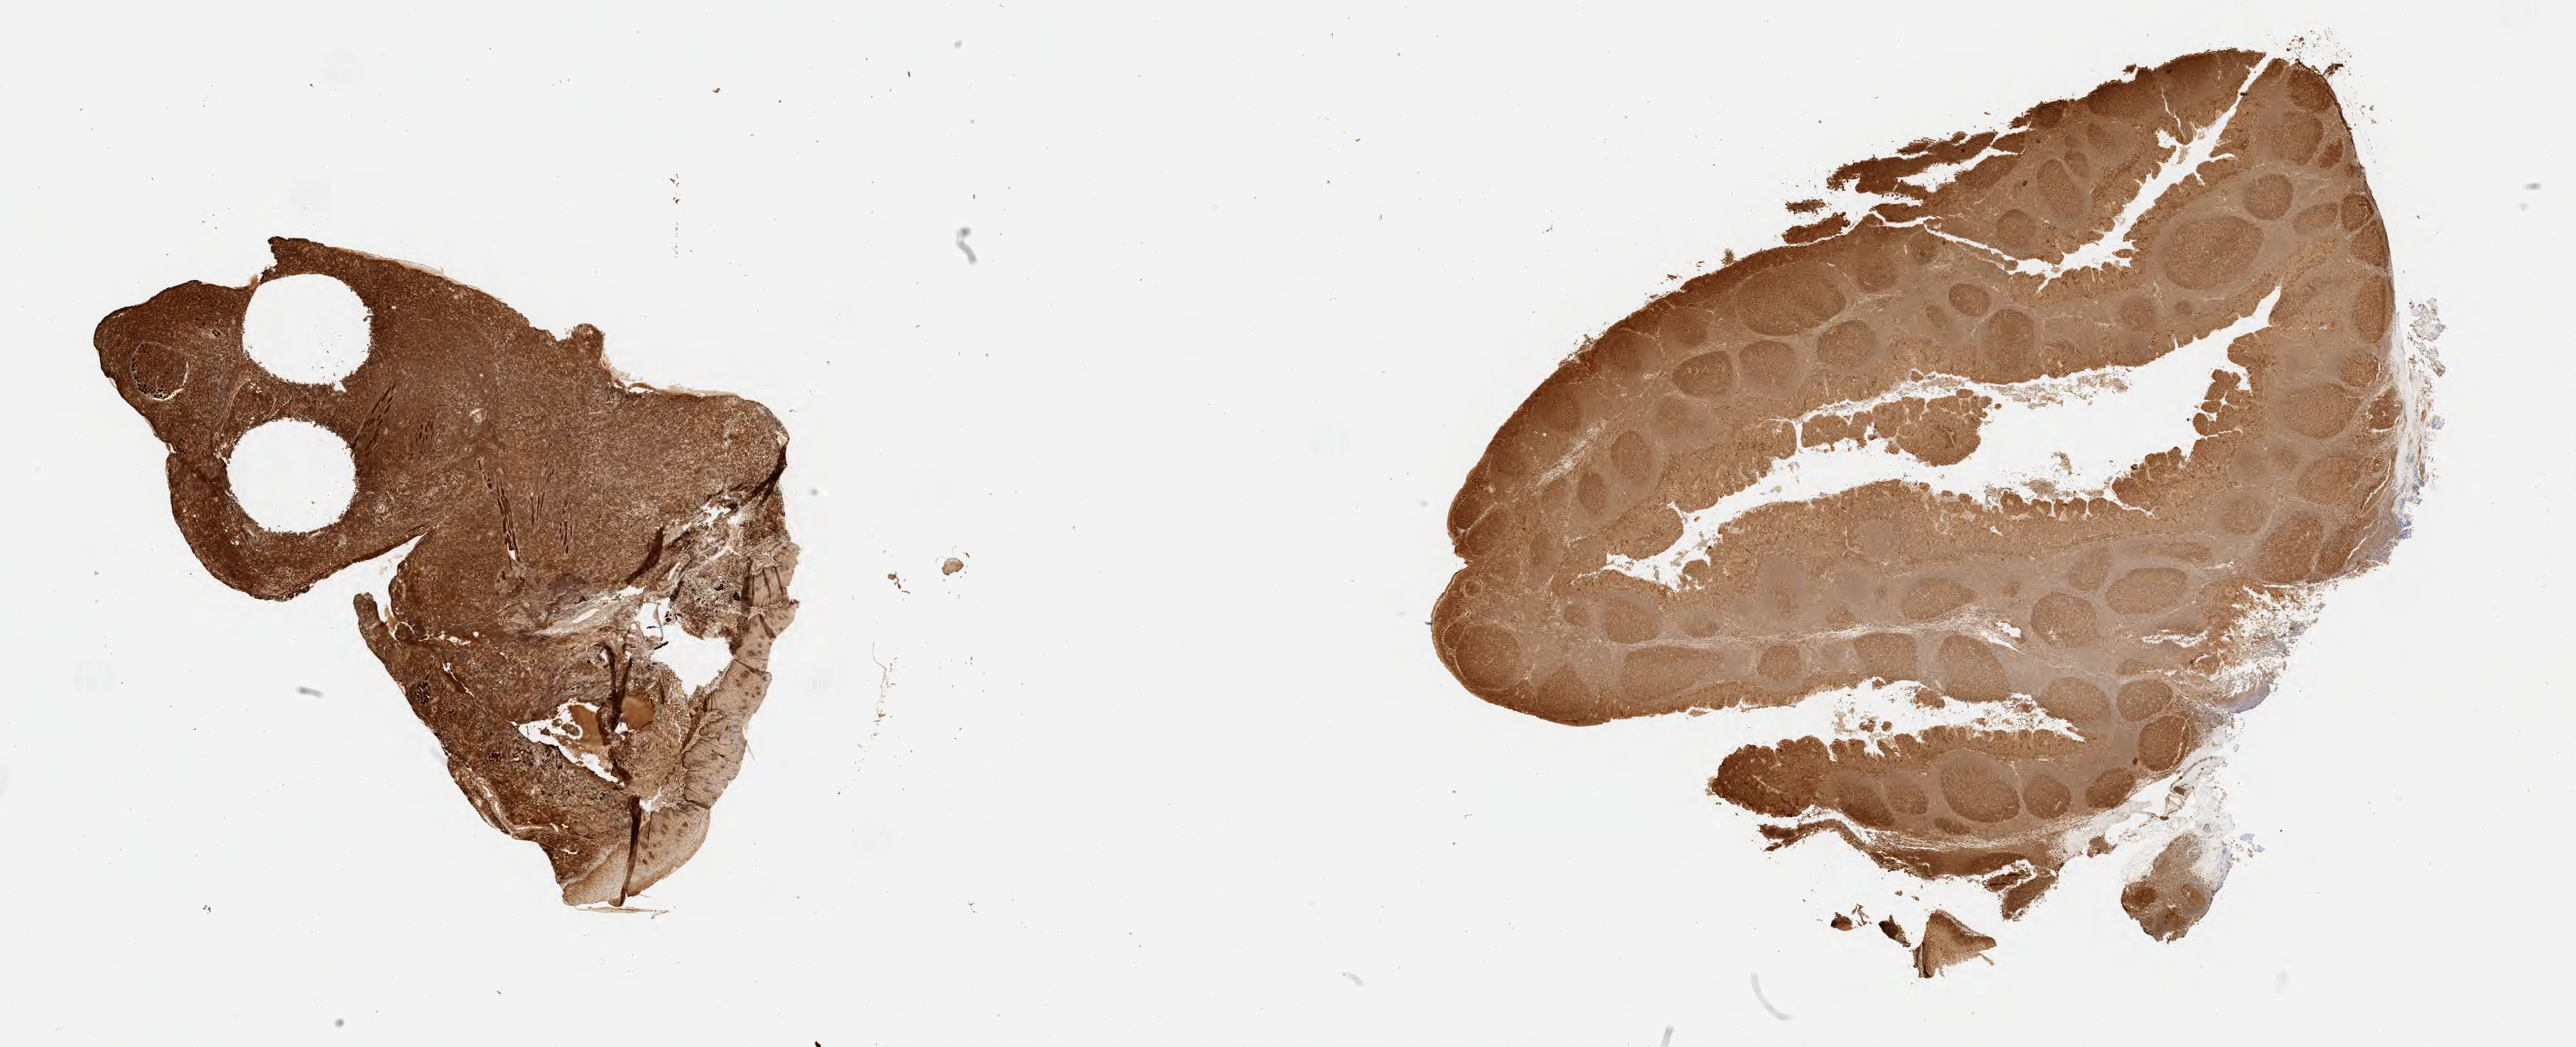
Immunohistochemistry (IHC) whole-slide image stained for BCL6, whole scanned area (about 30.2 x 12.3 mm) shown as a low-resolution overview, tumor tissue, site: cranium. Patient: male, age at initial diagnosis 6 years.
* histologic diagnosis: Burkitt lymphoma, NOS